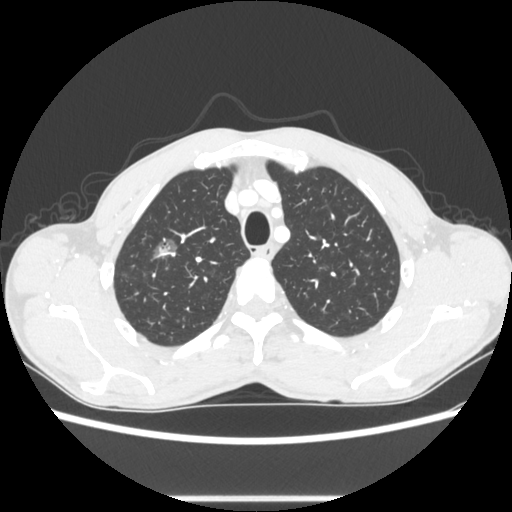
Chest CT, one axial slice; slice 231 of 289 in the series (ordered by position); reconstruction kernel STANDARD; 100 kVp; lung window (W 1500 / L -600 HU); 512 × 512 image matrix. Patient: male, 54 years. Case-level facts recorded for this patient, not image findings: clinical TNM (as recorded): T1a N0 M0.
Outlined on this slice (bounding box drawn by a radiologist):
- lung tumour (recorded histology: adenocarcinoma): bounding box <143,232,184,268> (left, top, right, bottom; pixels)